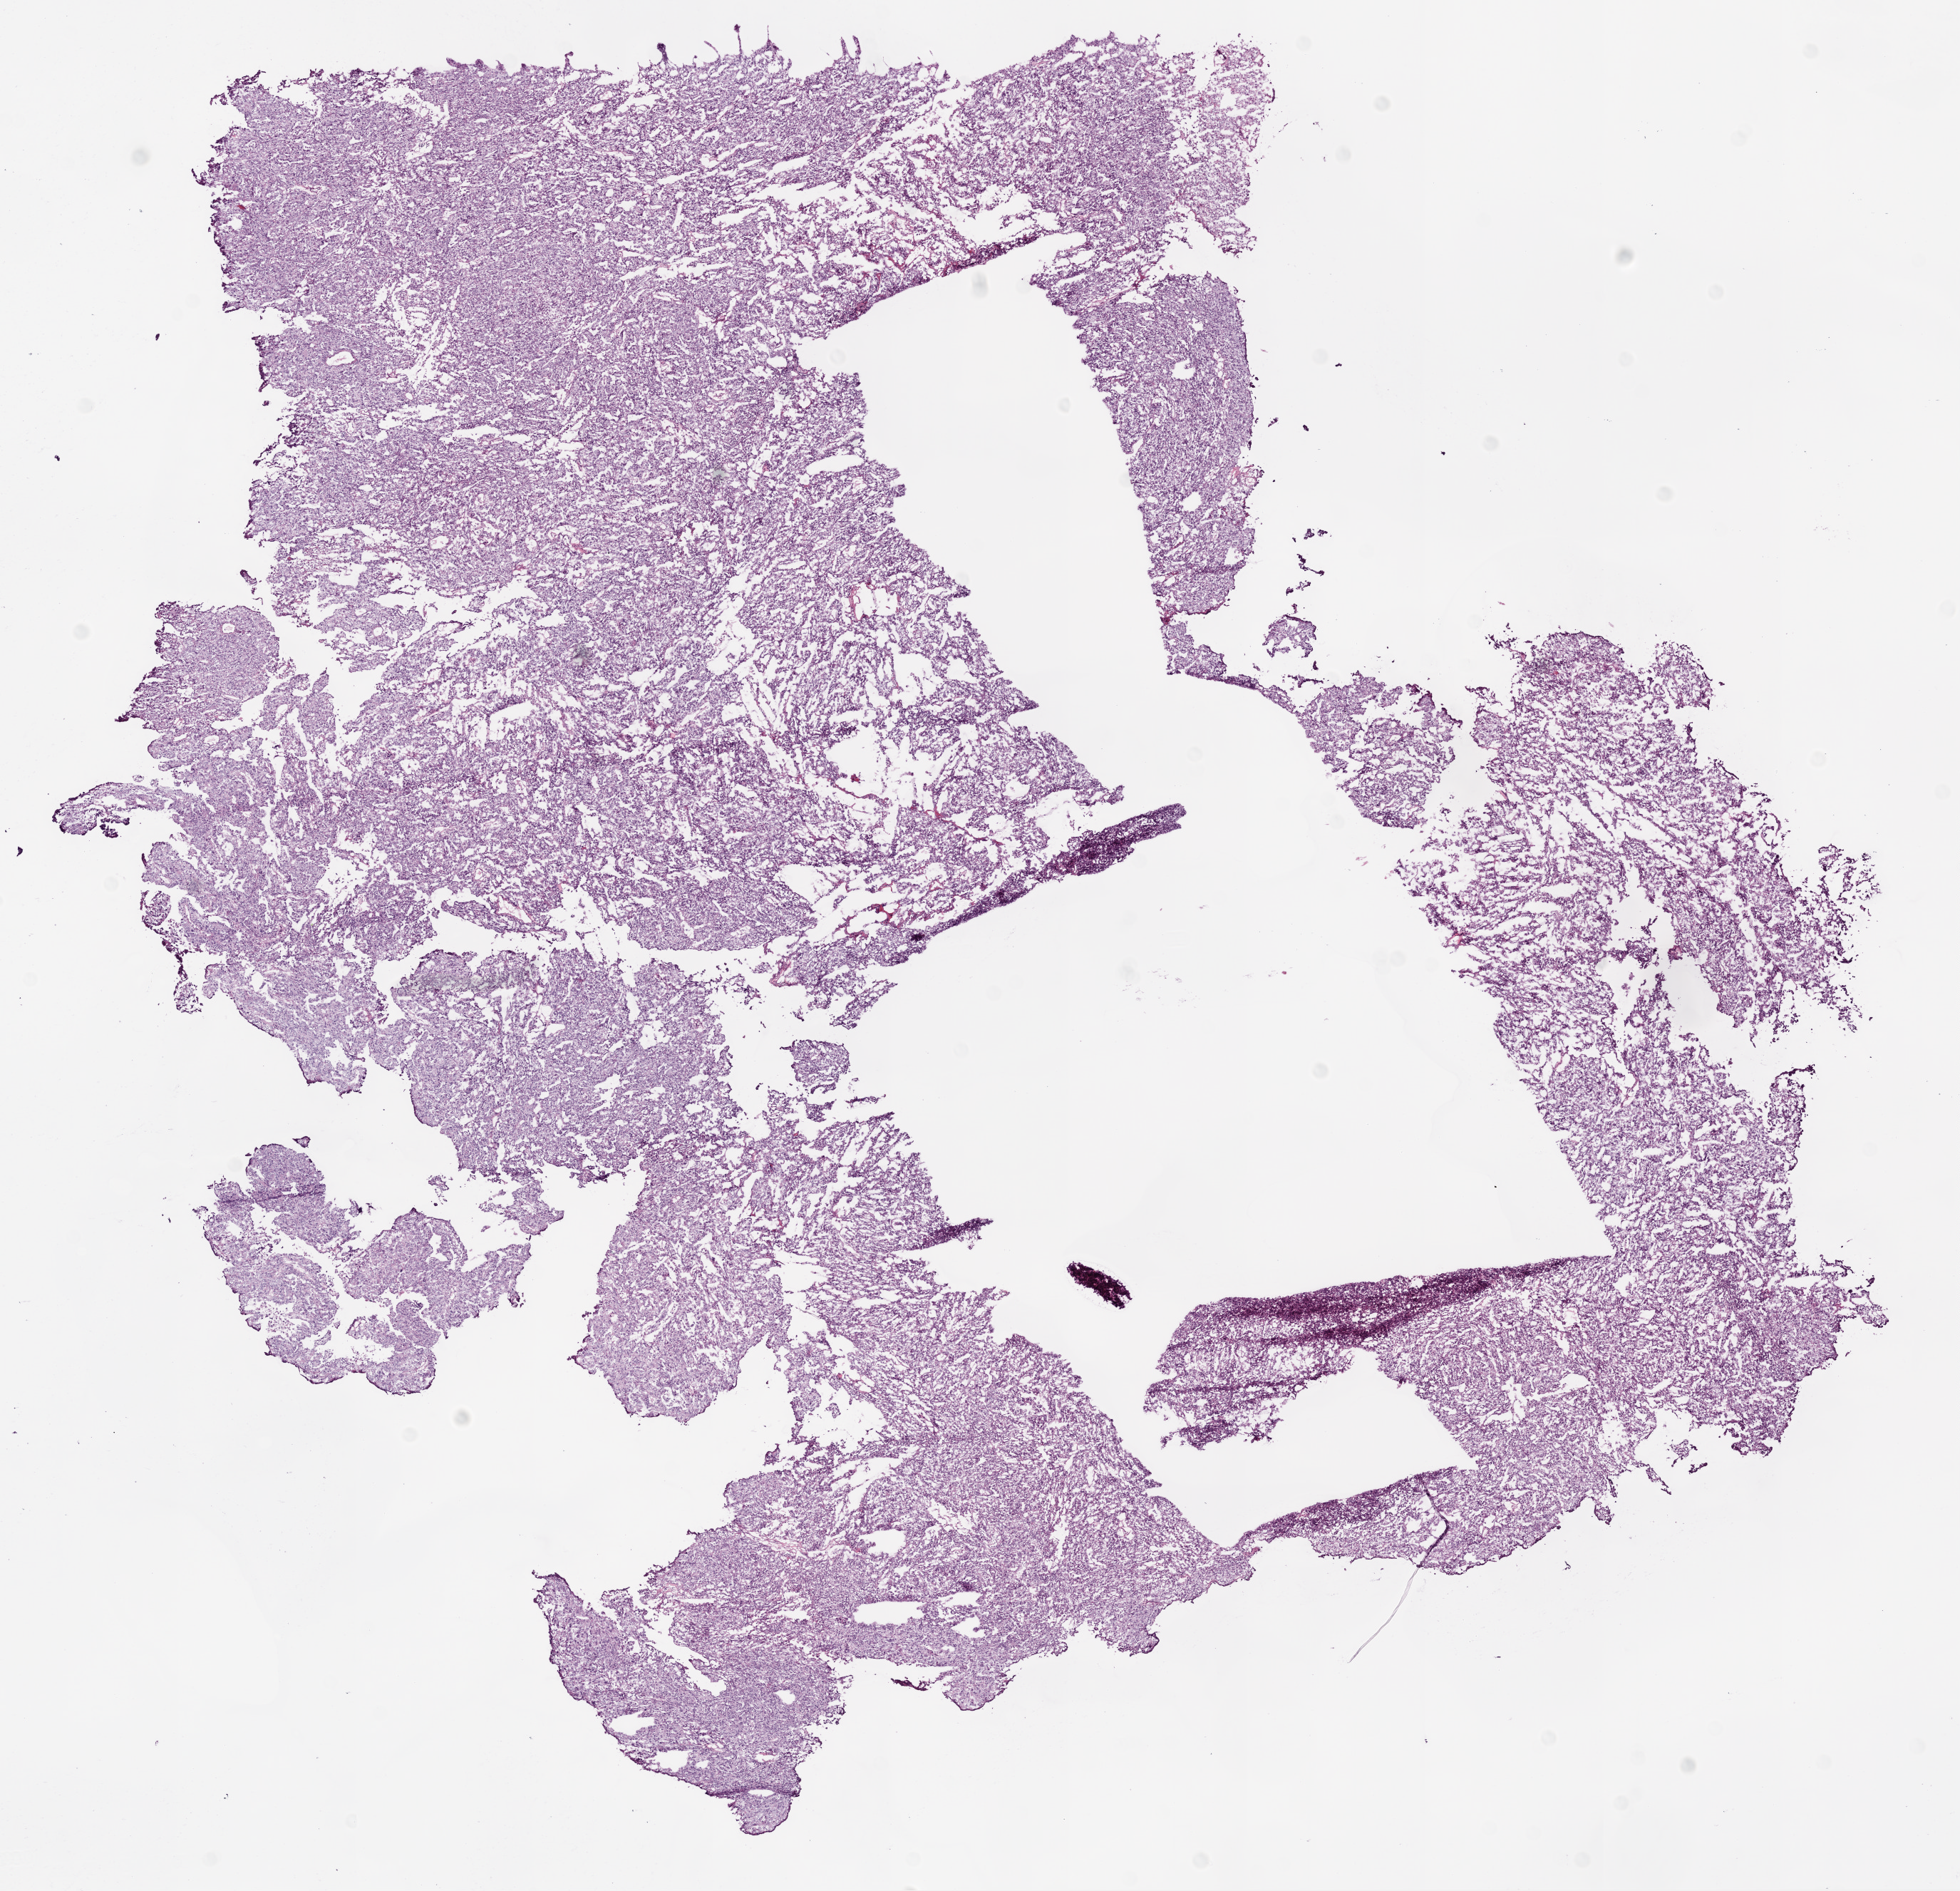
Hematoxylin and eosin (H&E) stained whole-slide image, shown as a low-resolution overview of the whole scanned area (about 11.0 x 10.6 mm, acquisition: 20x scan). Frozen section. Primary tumour sample from the ovary. Patient: female, age at initial diagnosis 41 years. Histologic grade: G3 (poorly differentiated). Slide review estimates, as recorded: tumour cells 98%, tumour nuclei 95%, normal cells 0%, stromal cells 0%, necrosis 2%.
Pathologic diagnosis: Serous cystadenocarcinoma, NOS. Laterality: left. FIGO stage: IIC.